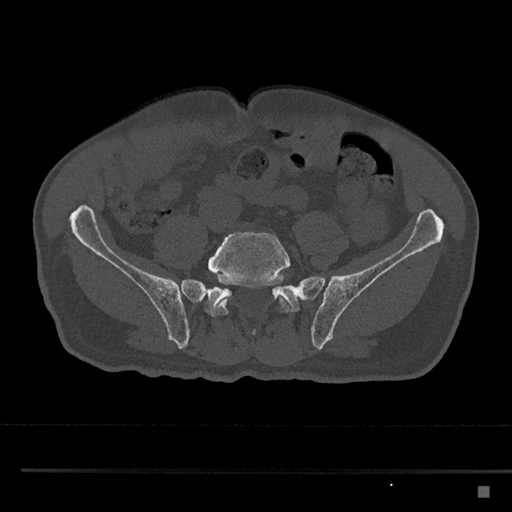
CT including the spine, one axial slice. Position 563 of 797 along the scan axis. Reconstruction kernel Br40s/3. Bone window (W 1800 / L 400 HU). 0.5 mm slice thickness. 512 × 512 image matrix. Male patient, age 59 years. From the clinical record (not read from this slice): primary cancer: prostate.
Structures marked on this image (semi-automatically segmented with operator editing):
- L5 vertebra: bounding box <208,232,291,335> (left, top, right, bottom; pixels)